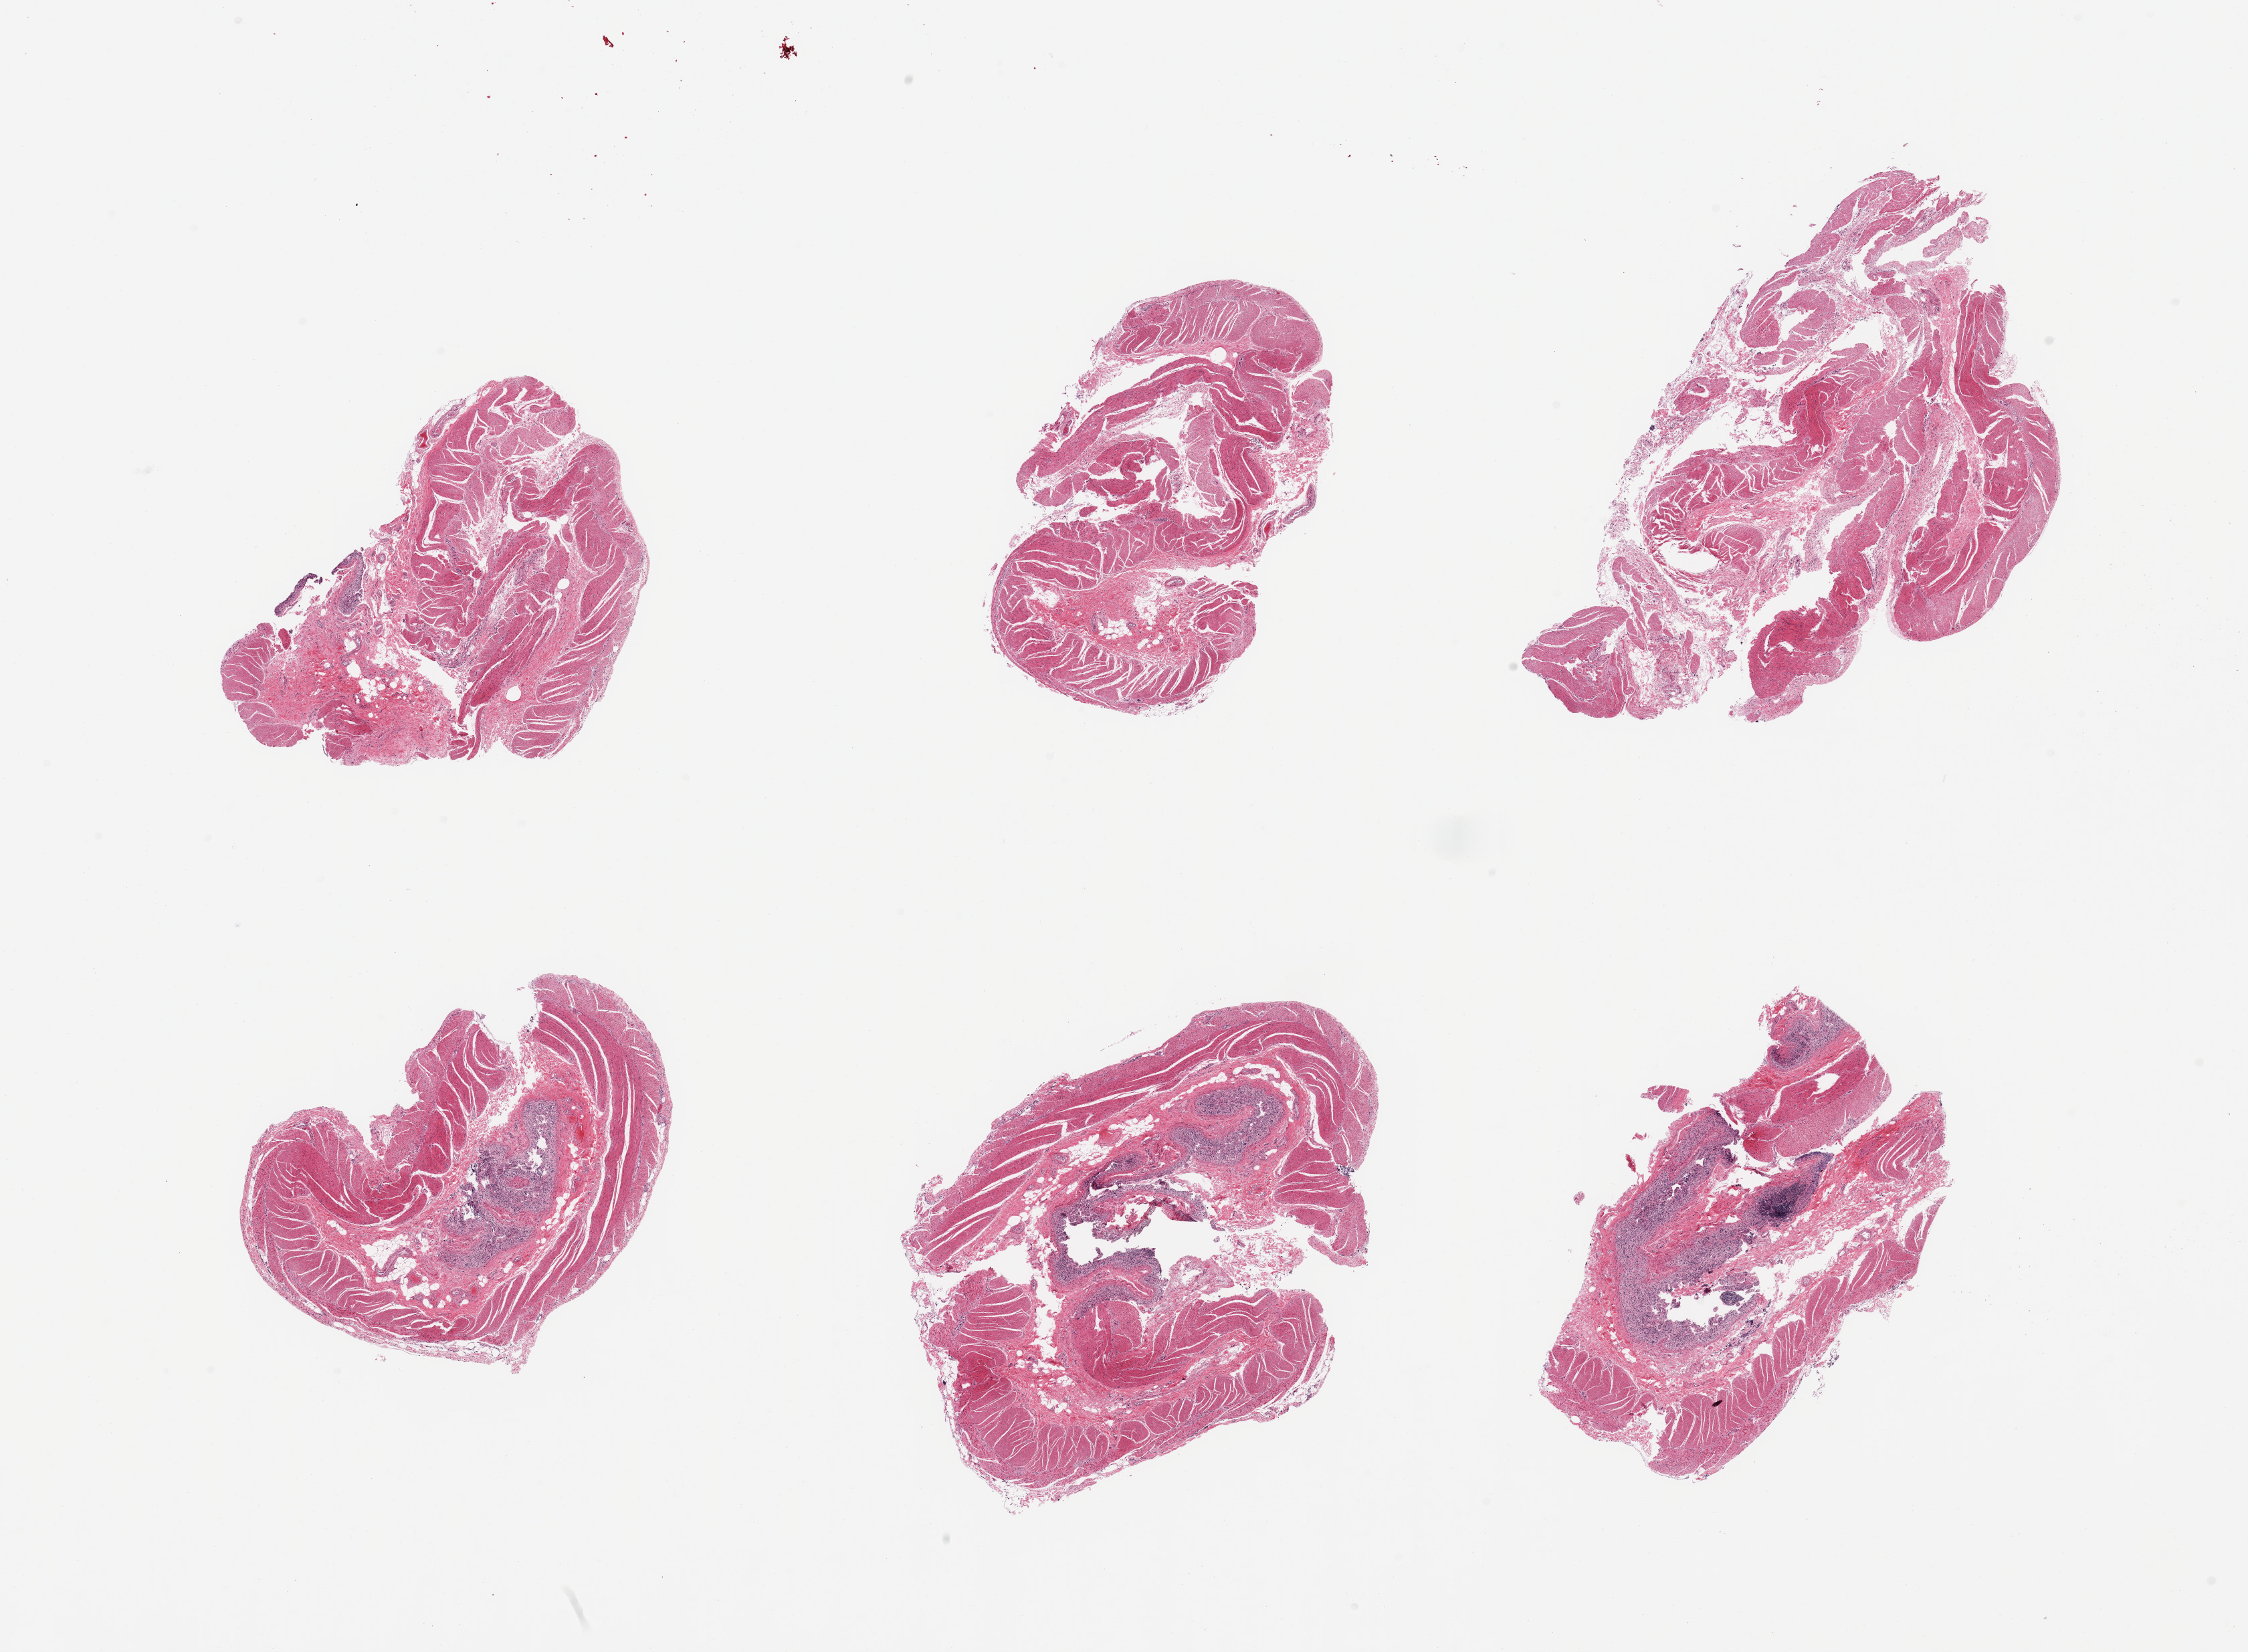
Digitized haematoxylin and eosin-stained section — whole scanned area (about 26.6 x 19.5 mm) shown as a low-resolution overview. PAXgene-fixed paraffin-embedded (PFPE) section. Target tissue: ileum. Tissue donor sample. Donor sex: female.
Review note (as recorded): 6 pieces, muscularis, trace autolyzed mucosa. Target lymphoid aggregates less than 1% of tissue.